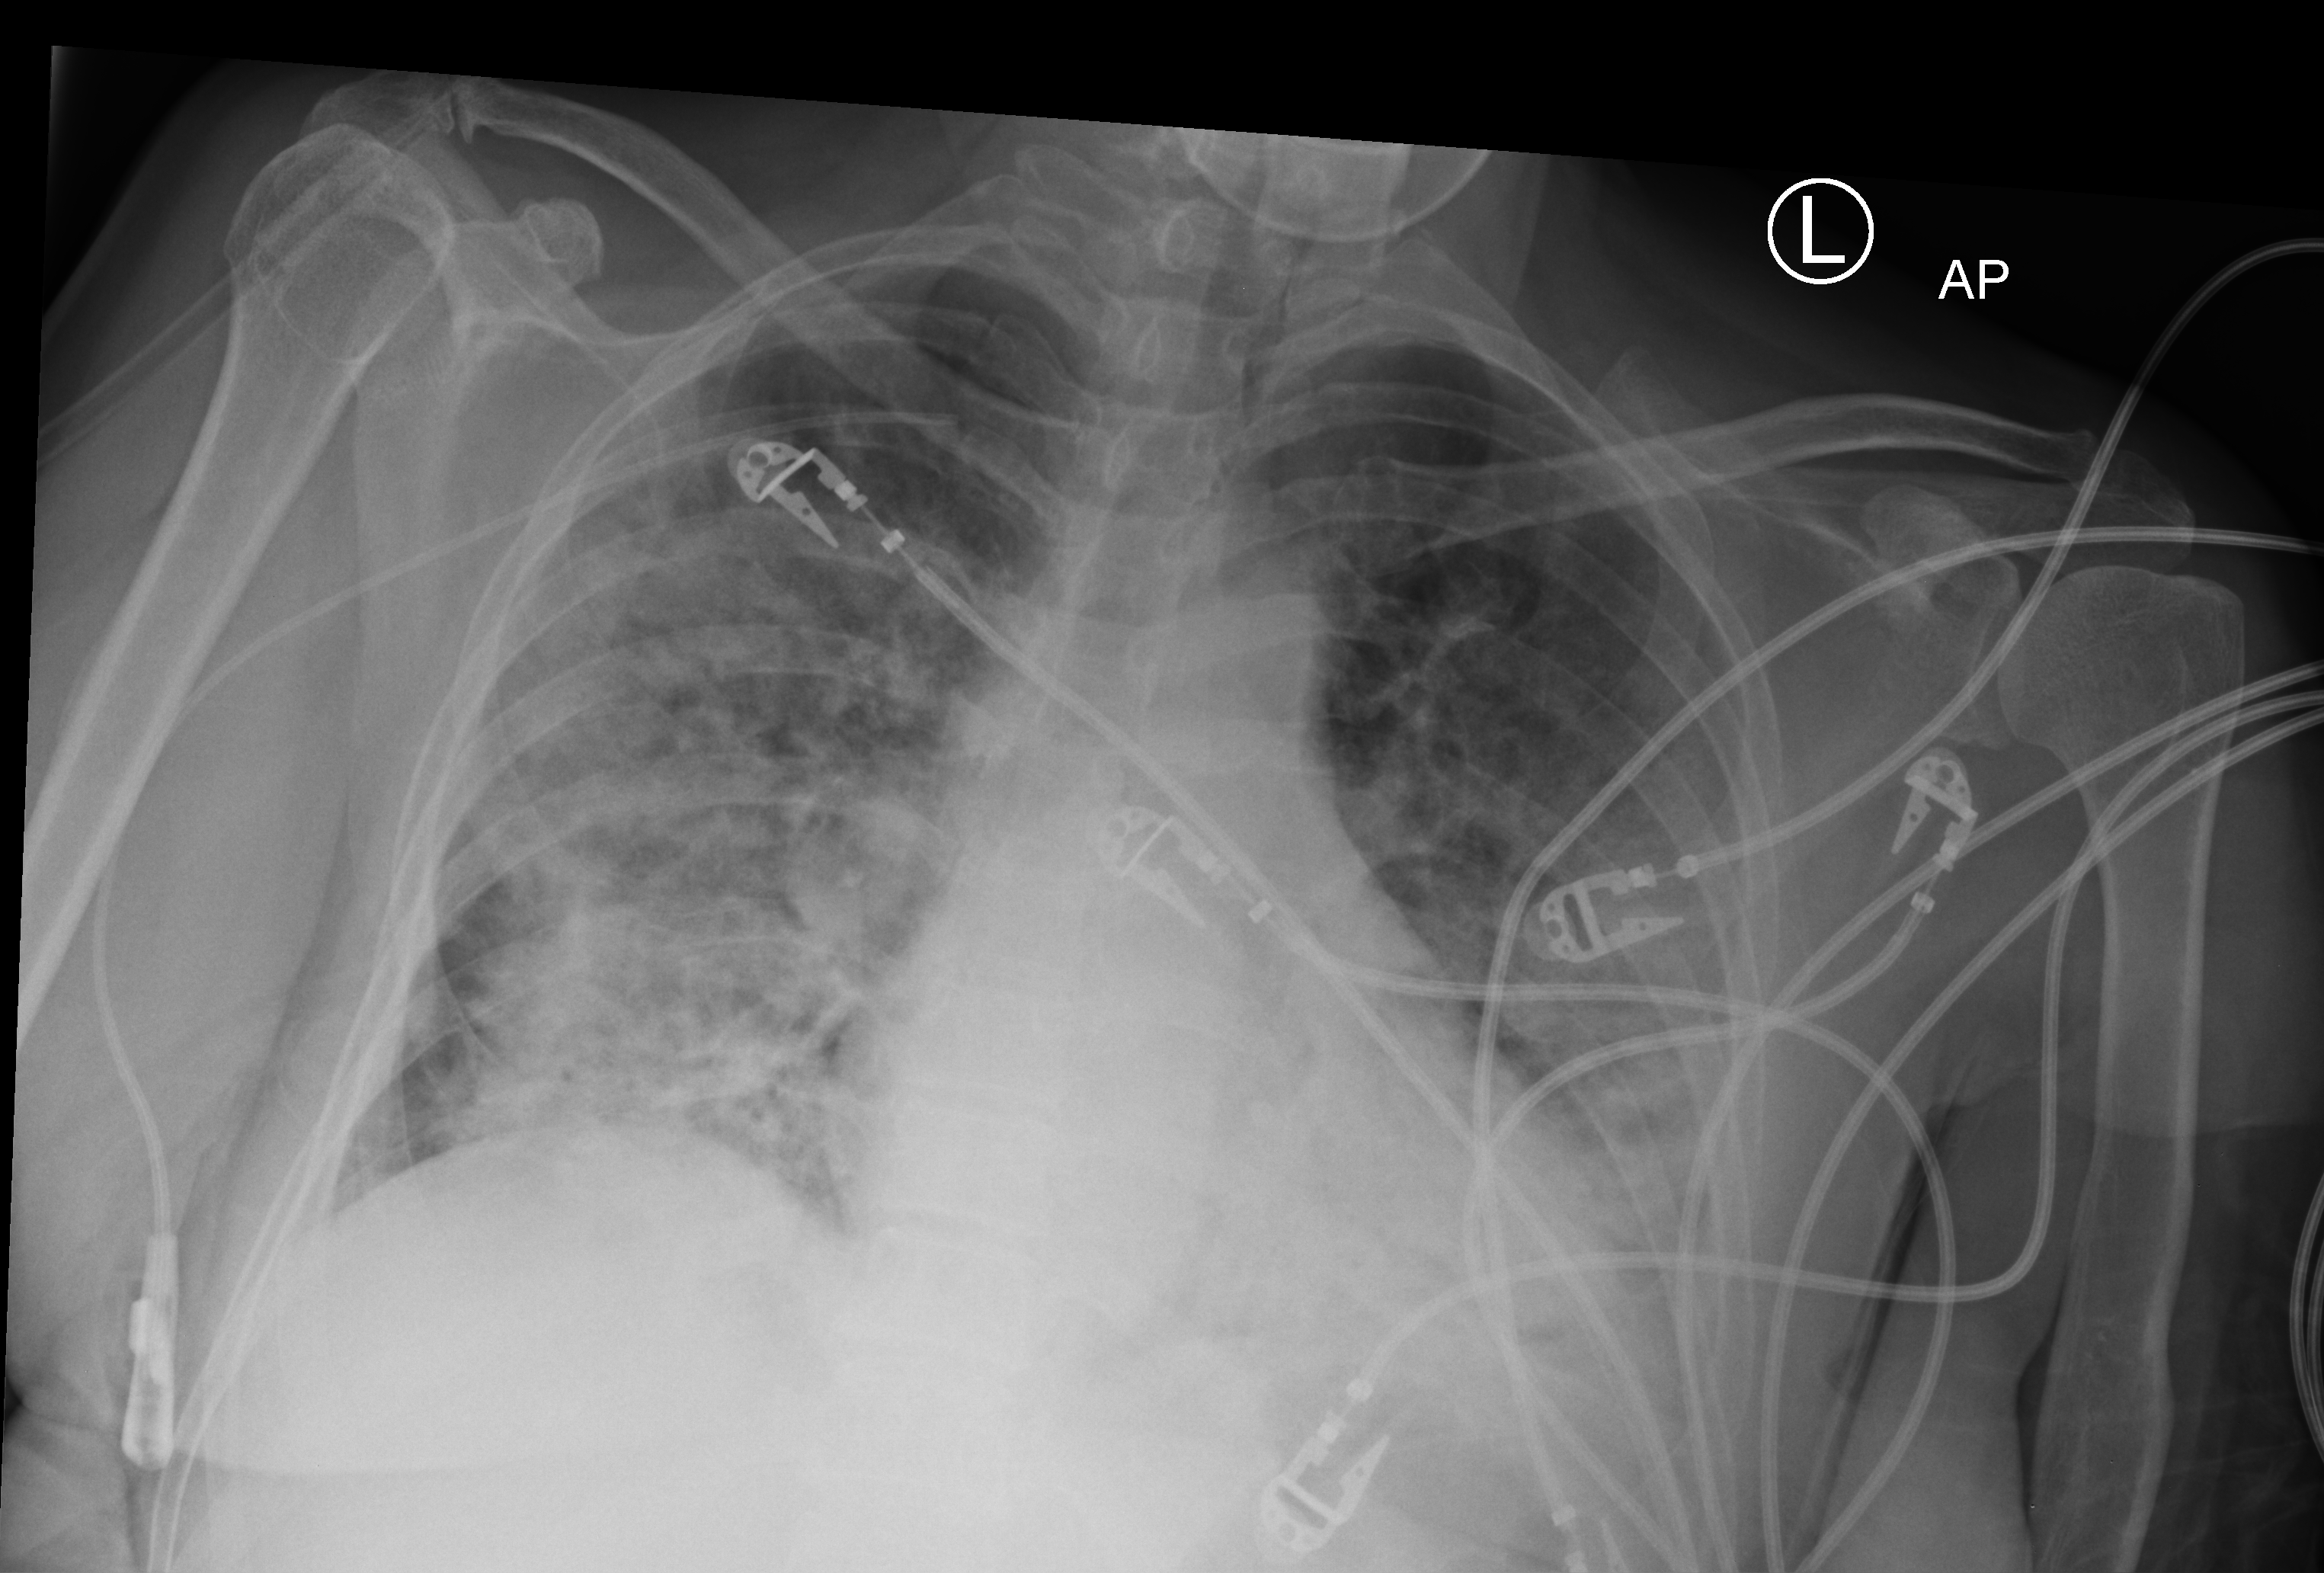
Portable chest radiograph; anteroposterior (AP) projection. Female patient hospitalised with COVID-19, age 60–74 years.
From the hospital-stay record, not from the radiograph (when in the stay this image was taken is not recorded):
- mechanically ventilated during this hospital stay: no
- length of hospital stay: 14 days
- admitted to intensive care during this hospital stay: yes